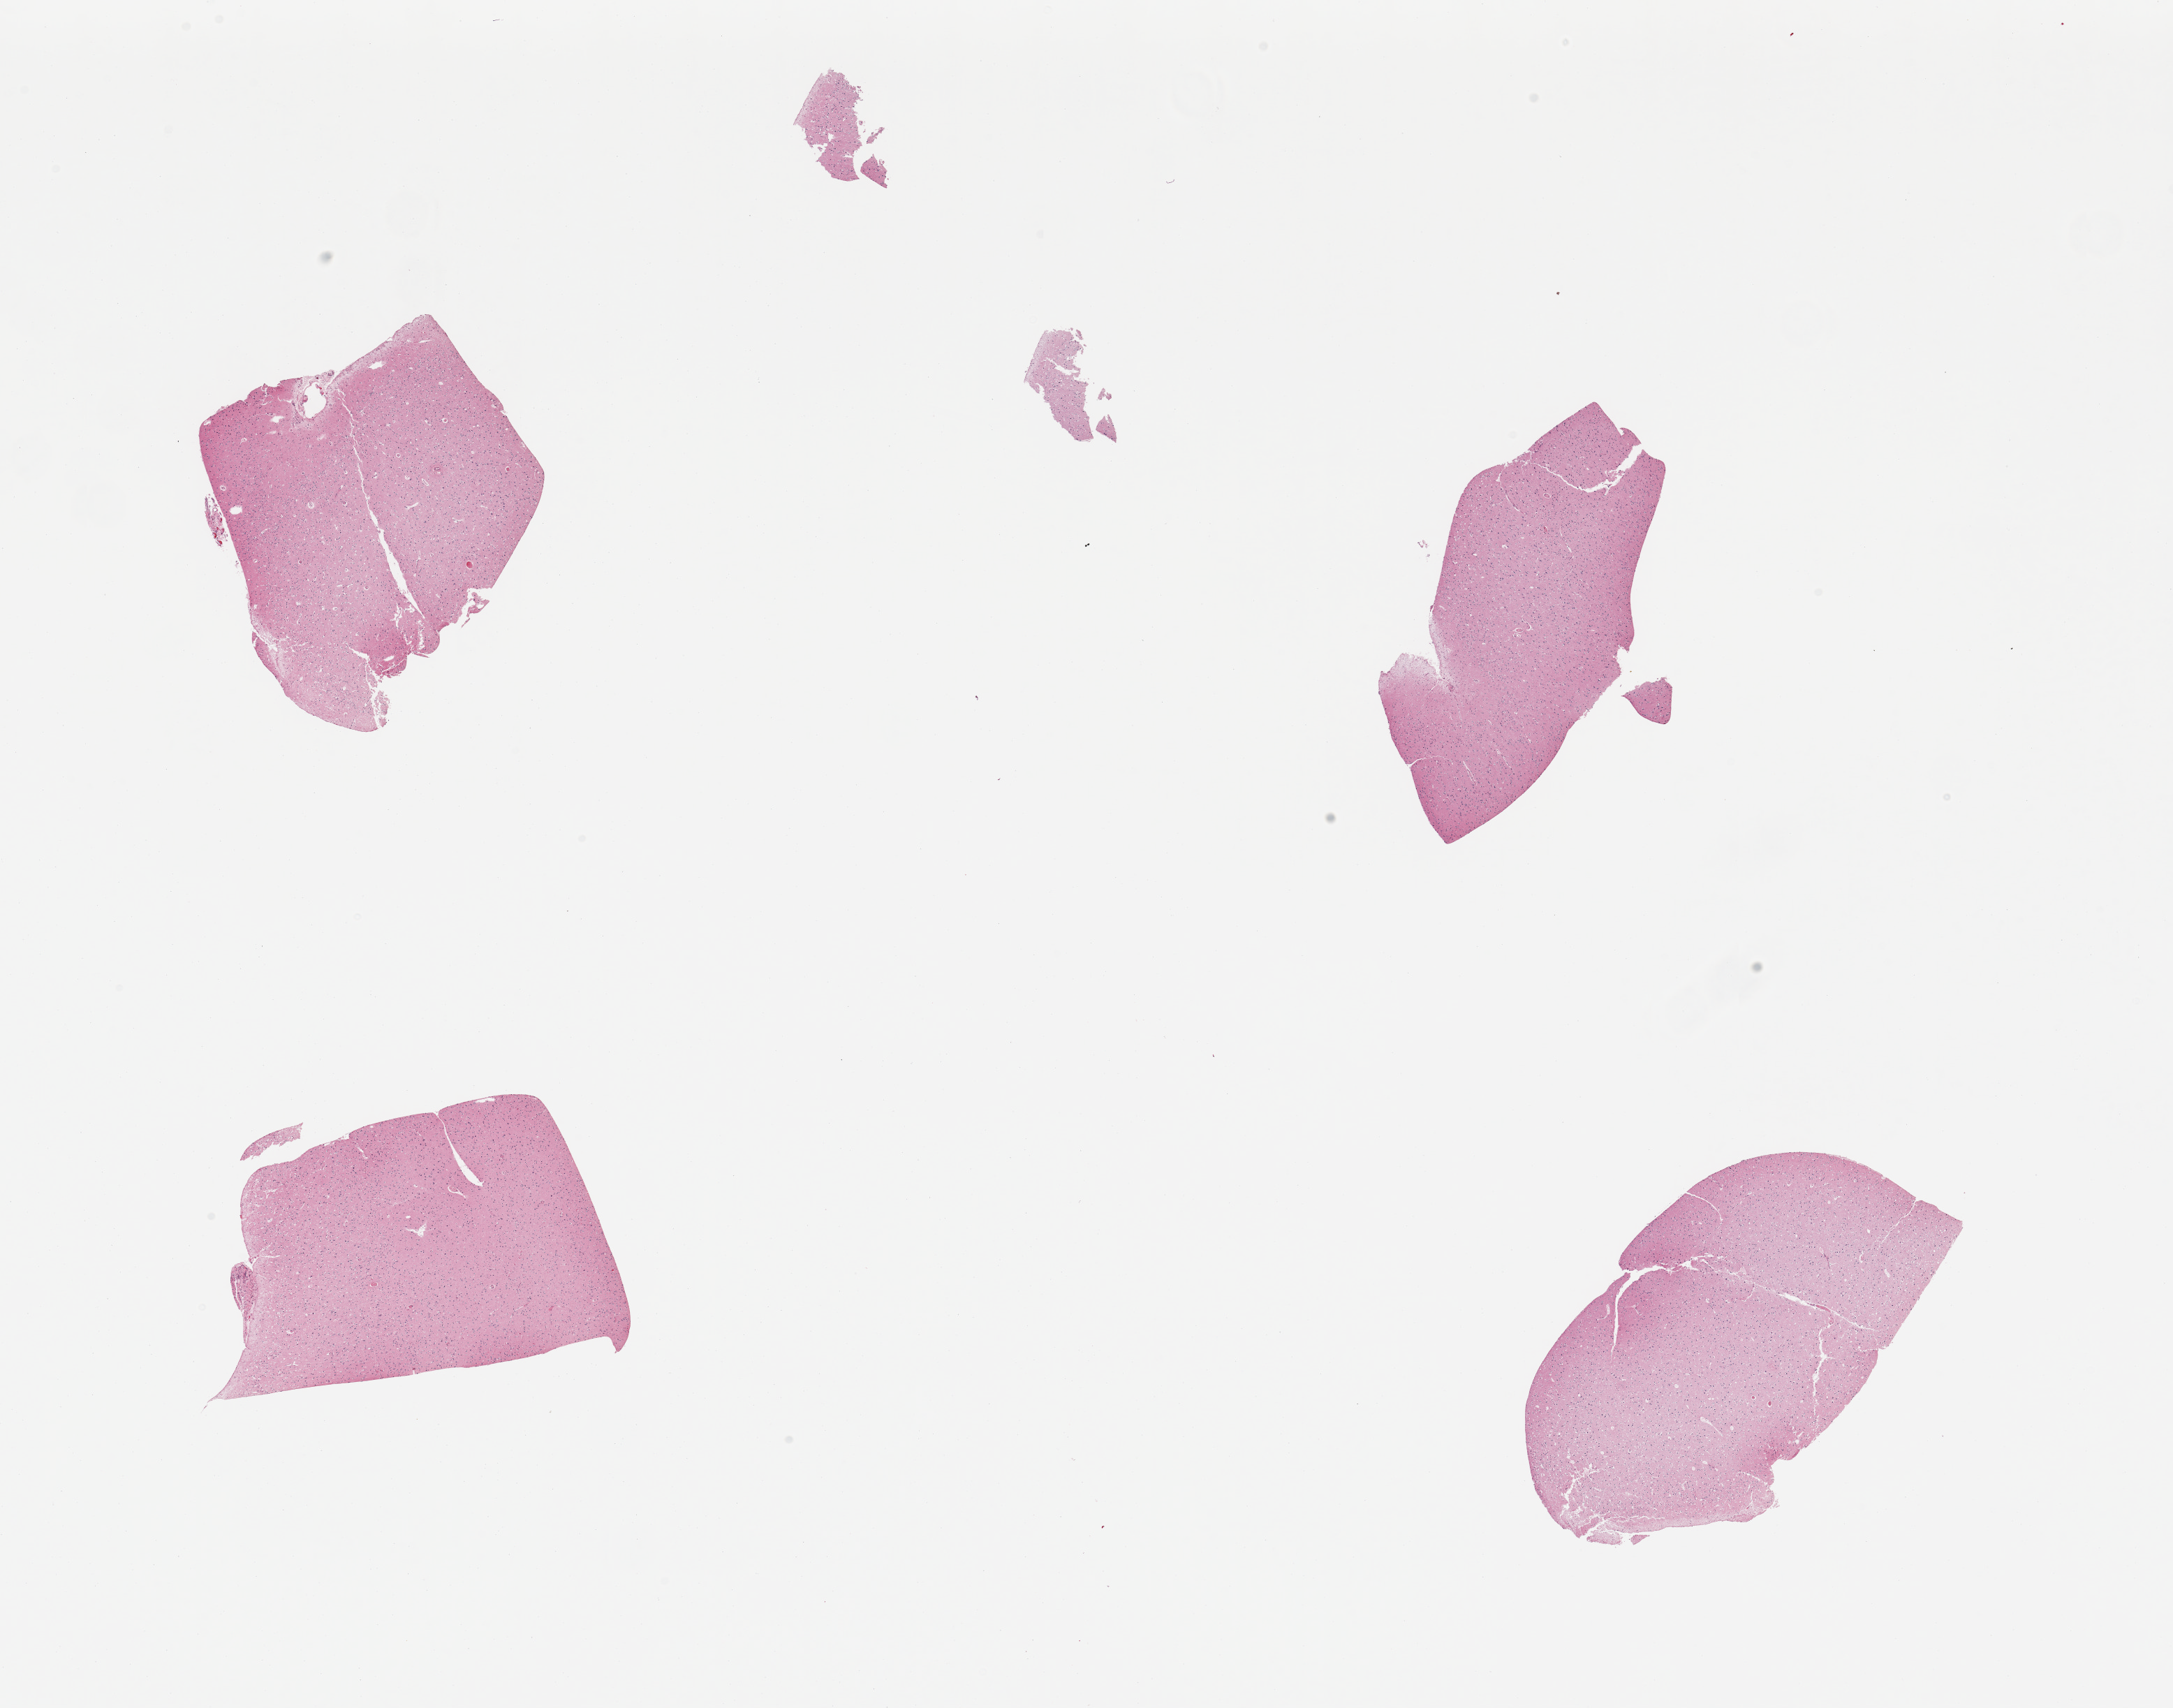
Whole-slide image, haematoxylin and eosin stain, low-resolution overview of the scanned area, about 24.6 x 19.3 mm (slide scanned at 20x). PAXgene-fixed, paraffin-embedded tissue. Sampled site (target tissue): cerebral cortex. Tissue donor sample. Male donor.
Reviewer comment on this tissue sample: 4 pieces.